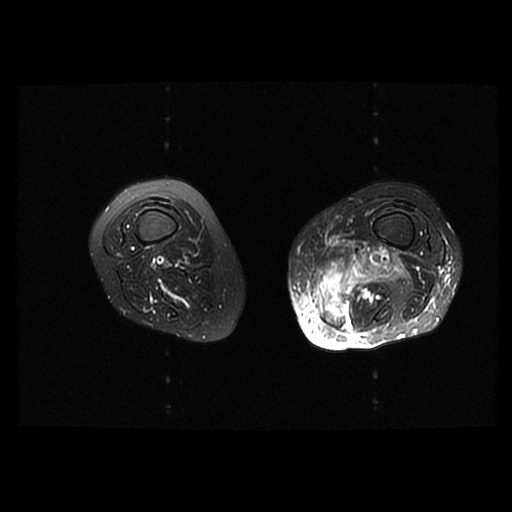
MRI of an extremity soft-tissue mass, one axial slice. Slice 21 of 42 in the series (ordered by position). T2-weighted fat-saturated. 6 mm slice thickness. 512 × 512 image matrix. Female patient. Case-level facts recorded for this patient, not image findings: histological type: pleomorphic leiomyosarcoma; grade: high; site of the primary tumour: left thigh.
Structures marked on this image (manually delineated by an expert):
- gross tumour volume including surrounding oedema: bounding box <307,246,404,330> (left, top, right, bottom; pixels)